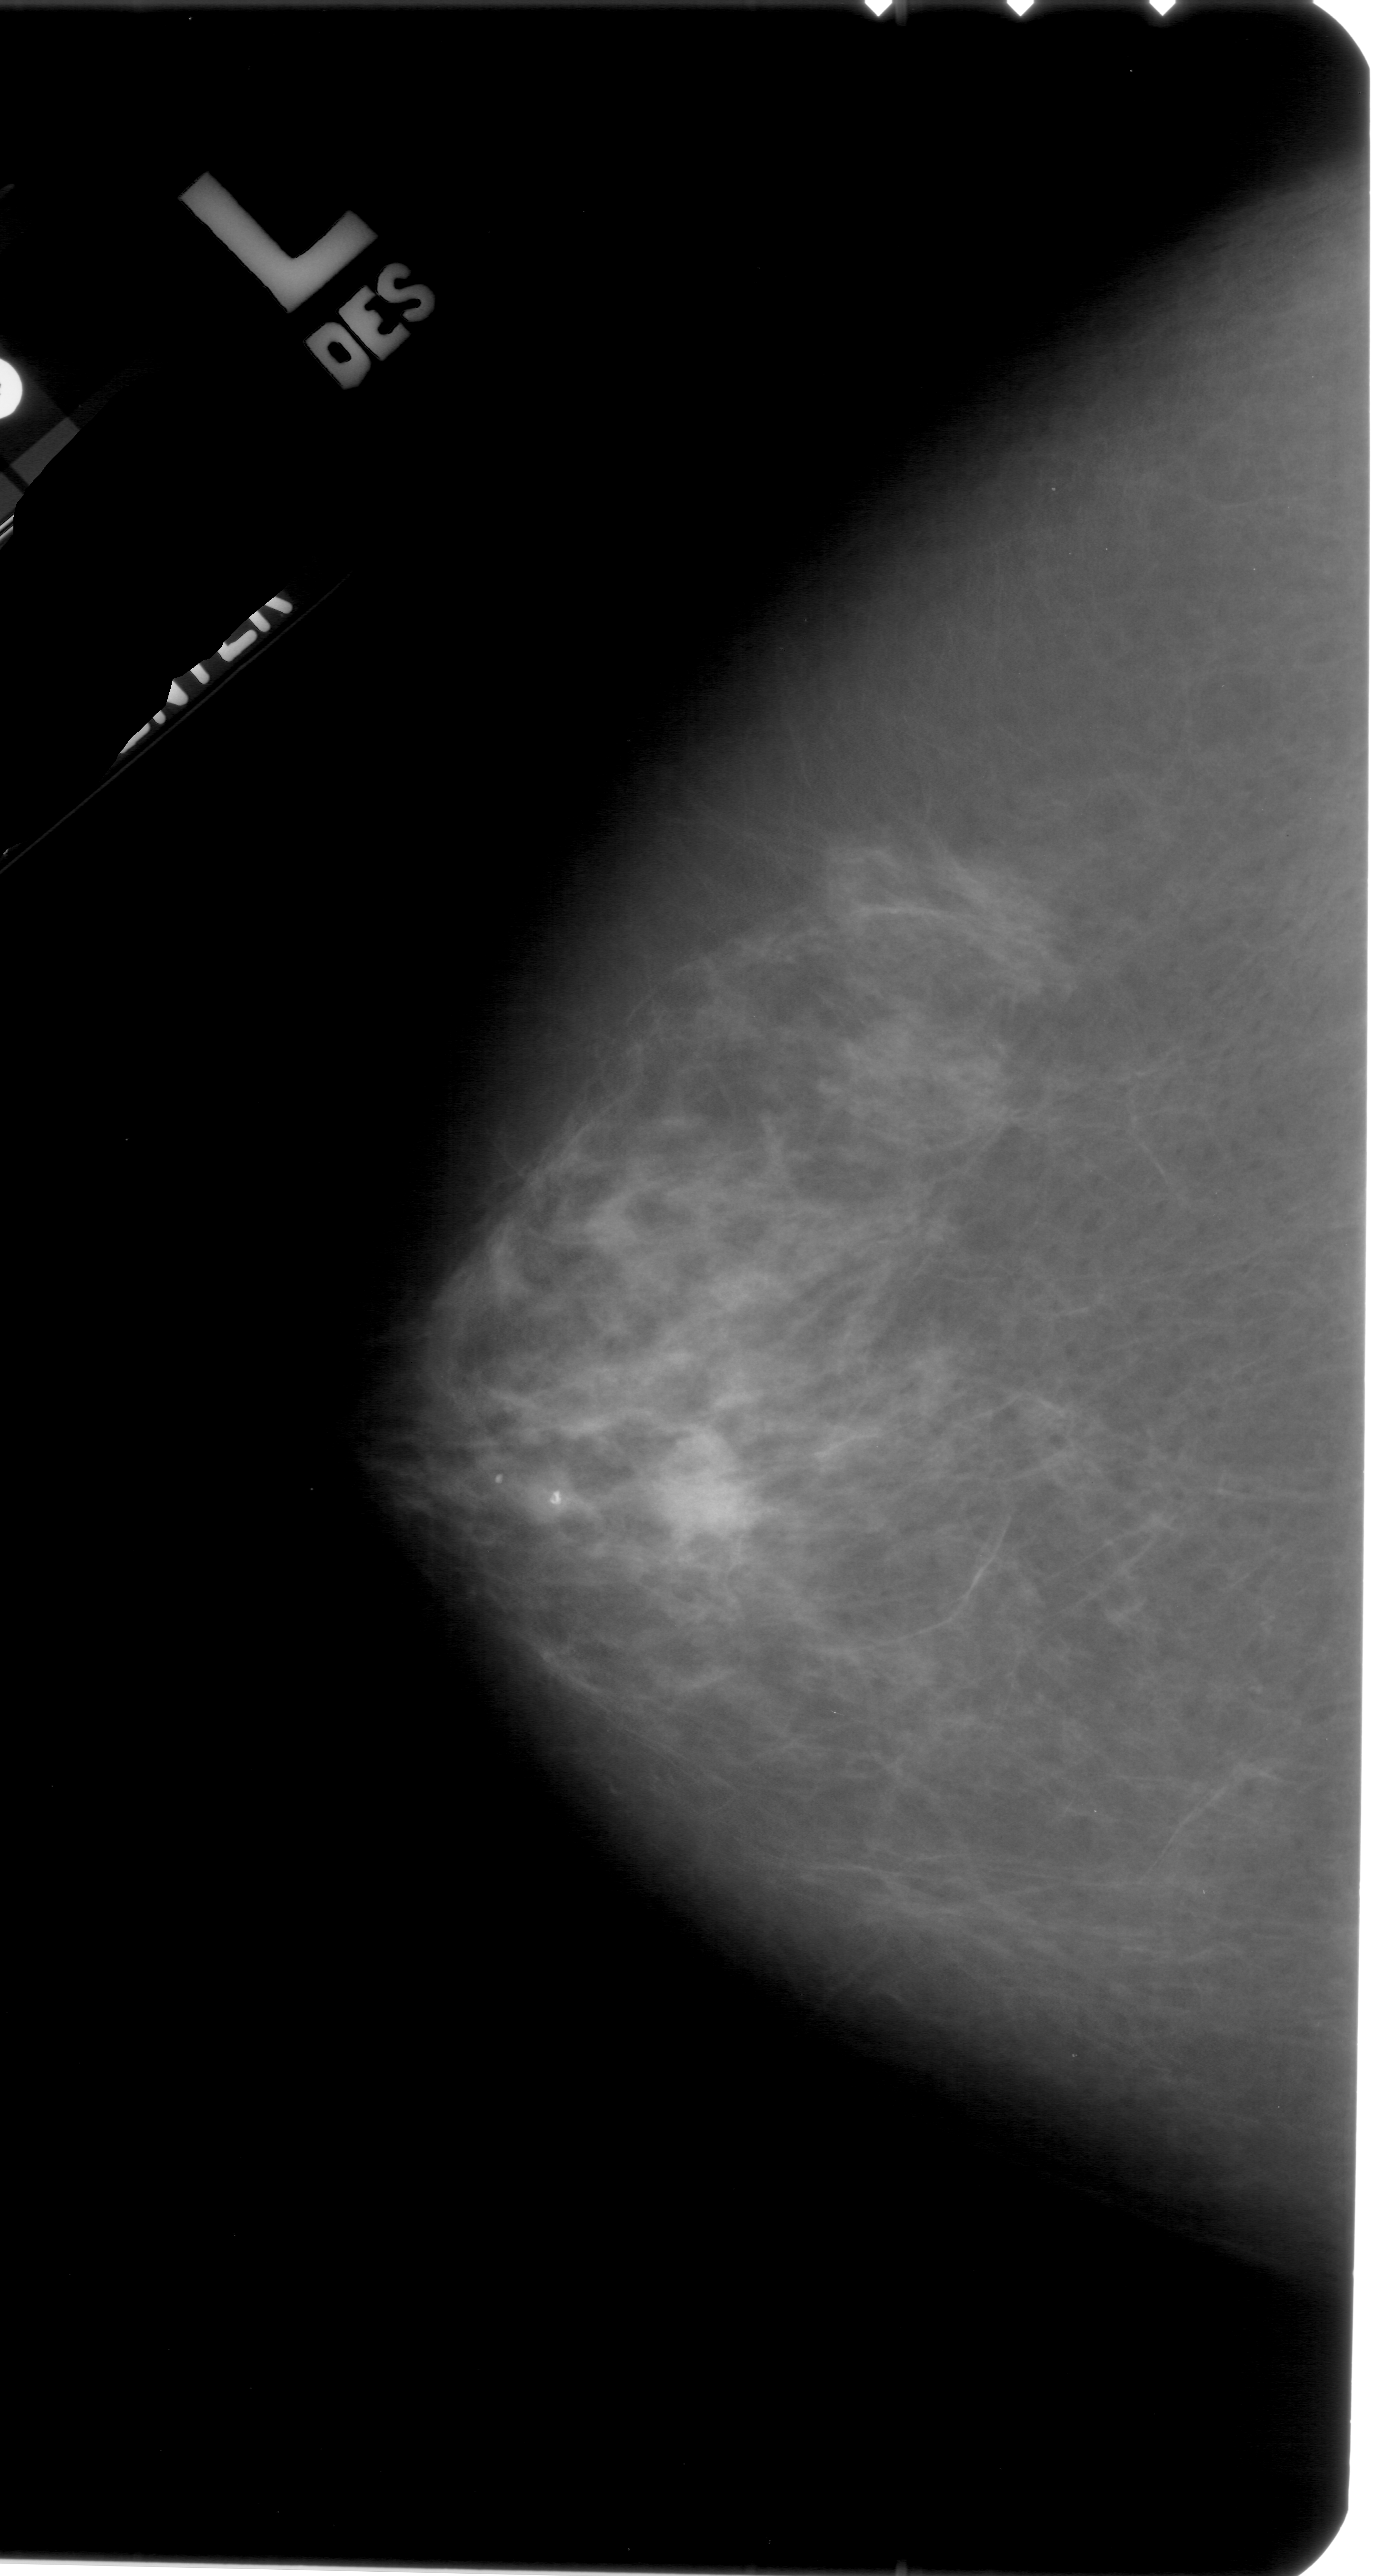
Digitized screen-film mammogram; left breast; CC view; BI-RADS breast density category 2 (scale 1–4); 1374 × 2576 image matrix.
Expert-marked regions of interest on this film, with their recorded descriptors:
- mass, shape irregular, margins ill defined; BI-RADS assessment category 4; subtlety rating 4 on a 1 (subtle) to 5 (obvious) scale; pathology result (as recorded, not read from the image): malignant: bounding box [x1, y1, x2, y2] px = [636, 1422, 766, 1542]